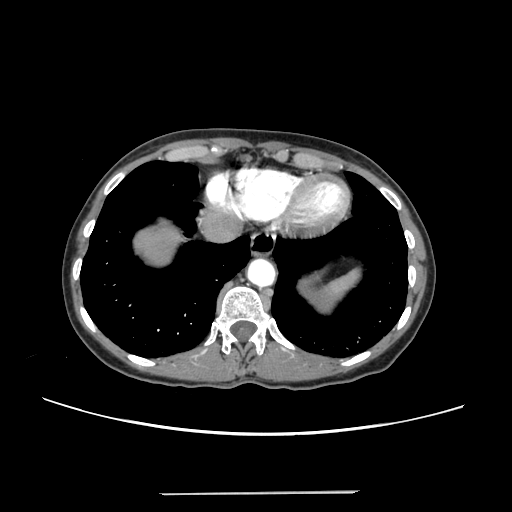
Contrast-enhanced abdominal CT, one axial slice. Position 224 of 240 along the scan axis. Intravenous contrast given. Soft-tissue window (W 400 / L 40 HU). 1.25 mm slice thickness. 512 × 512 image matrix, field of view 371 × 371 mm. Female patient, age 60 years. From the clinical record (not read from this slice): diagnosis: colorectal cancer liver metastases, imaged before liver resection; multiple liver metastases: no; largest metastasis: 1.5 cm; disease in both lobes: no.
Outlined on this slice (outlined manually by an expert reader):
- liver: bounding box <139,230,172,263> (left, top, right, bottom; pixels)
- planned liver remnant (the part of the liver to remain after resection): <139,229,172,263>